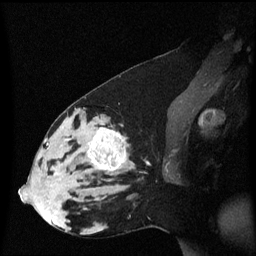
Breast MRI (dynamic contrast-enhanced), one sagittal slice. Position 30 of 60 along the scan axis. Dynamic contrast-enhanced series, image 2 of 3 at this slice position (ordered by acquisition). 1.5 T. TE 4.2 ms, TR 8.4 ms. 2 mm slice thickness. 256 × 256 image matrix, field of view 210 × 210 mm. Female patient, age 33 years. Case-level facts recorded for this patient, not image findings: setting: breast cancer imaged before/during neoadjuvant chemotherapy; receptor status: triple-negative.
Structures marked on this image (semi-automatic segmentation, software-assisted and operator-edited):
- analysis volume of interest (the breast-tissue region the enhancement analysis was run in; not a lesion): bounding box <44,123,136,189> (left, top, right, bottom; pixels)
- tumour enhancement mask (voxels above the 70 % enhancement threshold inside the analysis volume of interest): <55,128,127,176>